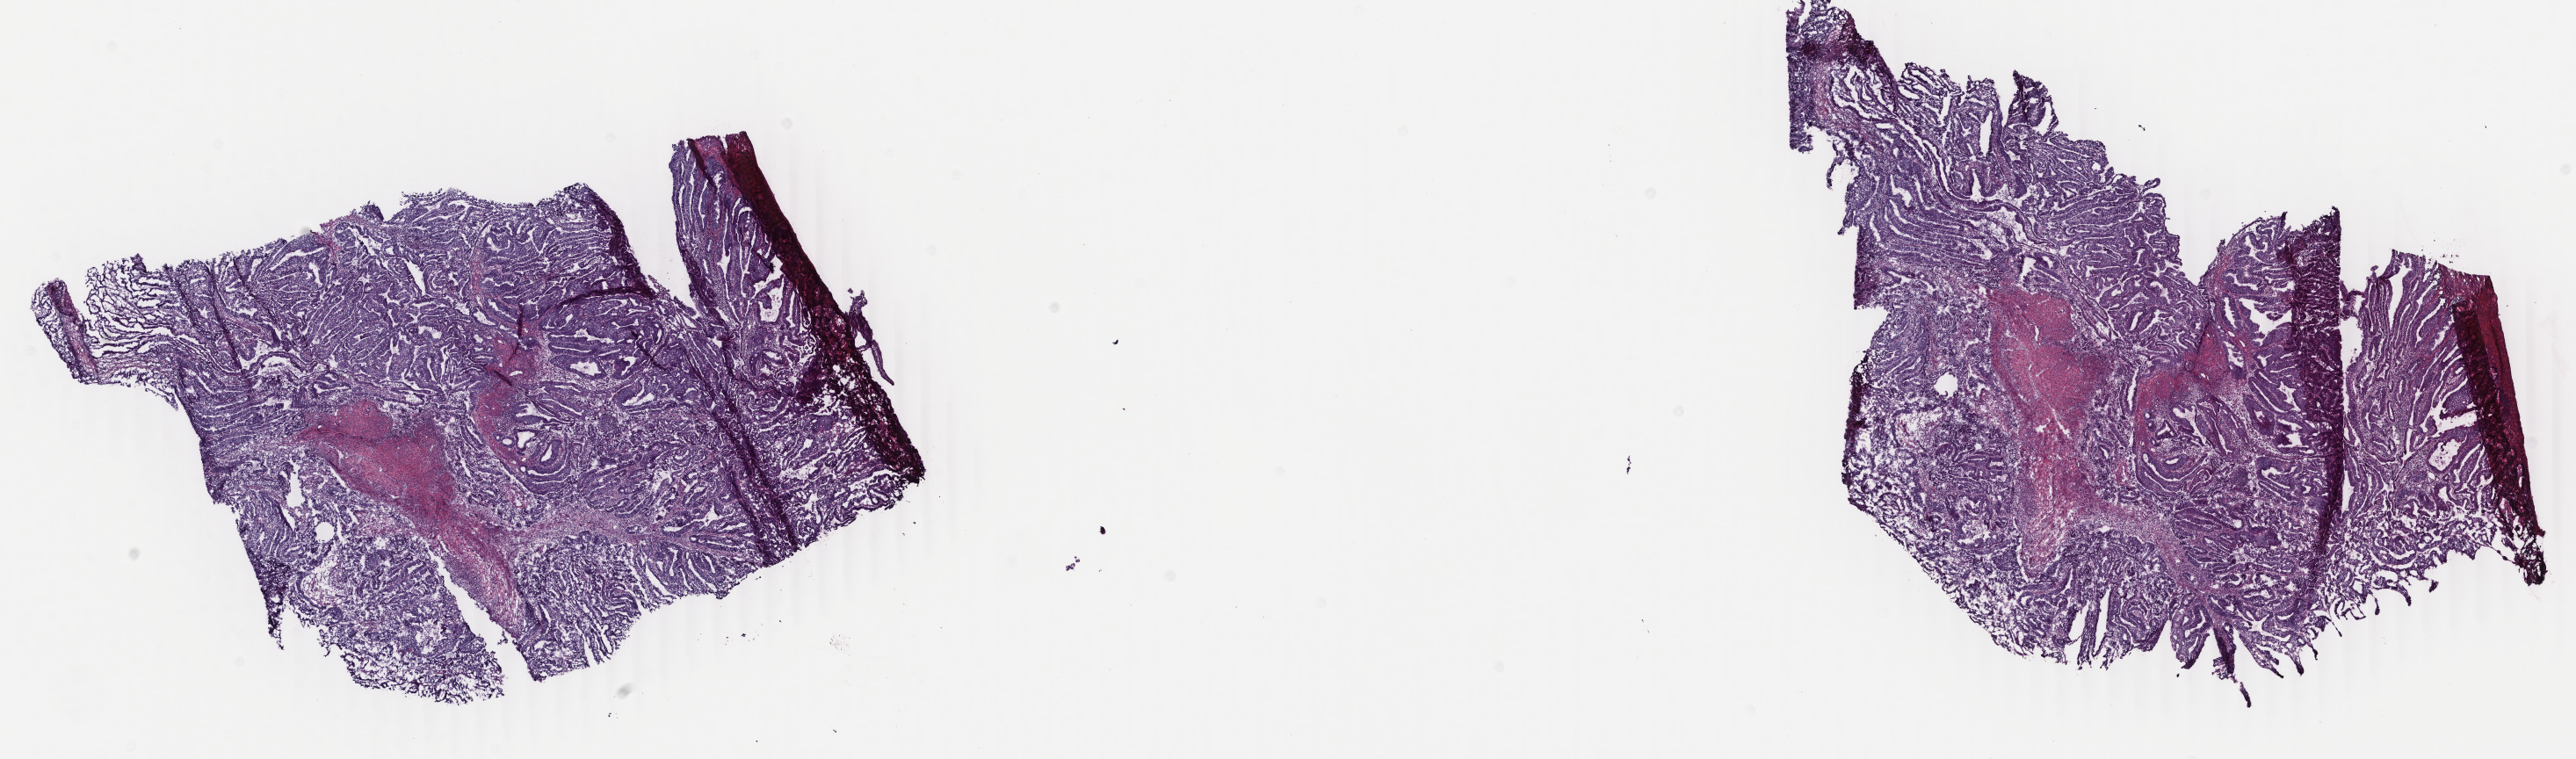
Digitized H&E-stained tissue section (whole slide) — a low-resolution overview of the entire scanned area, about 23.3 x 6.9 mm; frozen section; uterus, primary tumour sample. Female patient; age at initial diagnosis 64 years. Histologic grade: G2 (moderately differentiated). Pathologist review of this section (percent, as recorded): tumour cells 90%, tumour nuclei 70%, normal cells 0%, stromal cells 10%, necrosis 0%. Infiltration values recorded for this section: lymphocyte infiltration 0%, monocyte infiltration 0%, neutrophil infiltration 0%.
- diagnosis: Endometrioid adenocarcinoma, NOS (endometrium)
- FIGO stage: IB